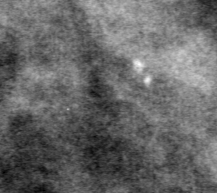
Crop from a digitized film mammogram around one marked abnormality, right breast, MLO view.
Finding: calcifications, morphology pleomorphic, distribution clustered; BI-RADS assessment category 3; pathology (as recorded): benign.